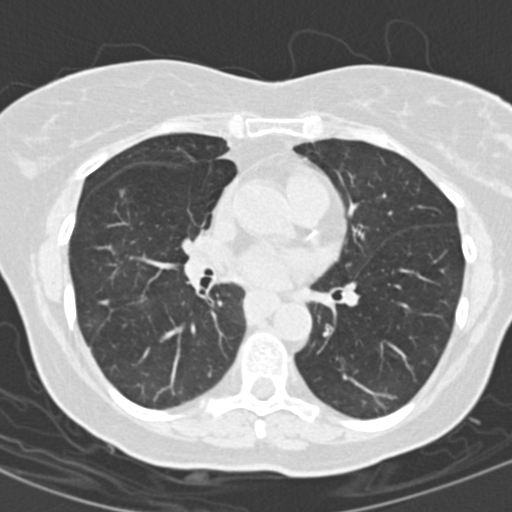
Low-dose screening chest CT, one axial slice. Position 76 of 154 along the scan axis. Lung window (W 1500 / L -600 HU). 2 mm slice thickness. 512 × 512 image matrix, field of view 280 × 280 mm.
Annotated regions visible in this slice (outlined manually by an expert reader):
- lesion 2 (nodule, middle lobe of right lung): bounding box [x1, y1, x2, y2] px = [120, 187, 128, 198]